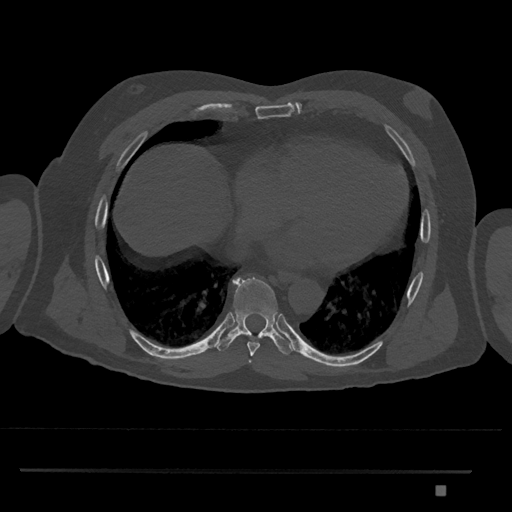
CT including the spine, one axial slice. Slice 1130 of 1134 in the series (ordered by position). Reconstruction kernel Br40s/3. 120 kVp. Bone window (W 1800 / L 400 HU). 512 × 512 image matrix, field of view 429 × 429 mm. Male patient, age 65 years. Case-level facts recorded for this patient, not image findings: primary cancer: prostate.
Outlined on this slice (semi-automatic segmentation, software-assisted and operator-edited):
- T8 vertebra: bounding box <216,277,295,356> (left, top, right, bottom; pixels)